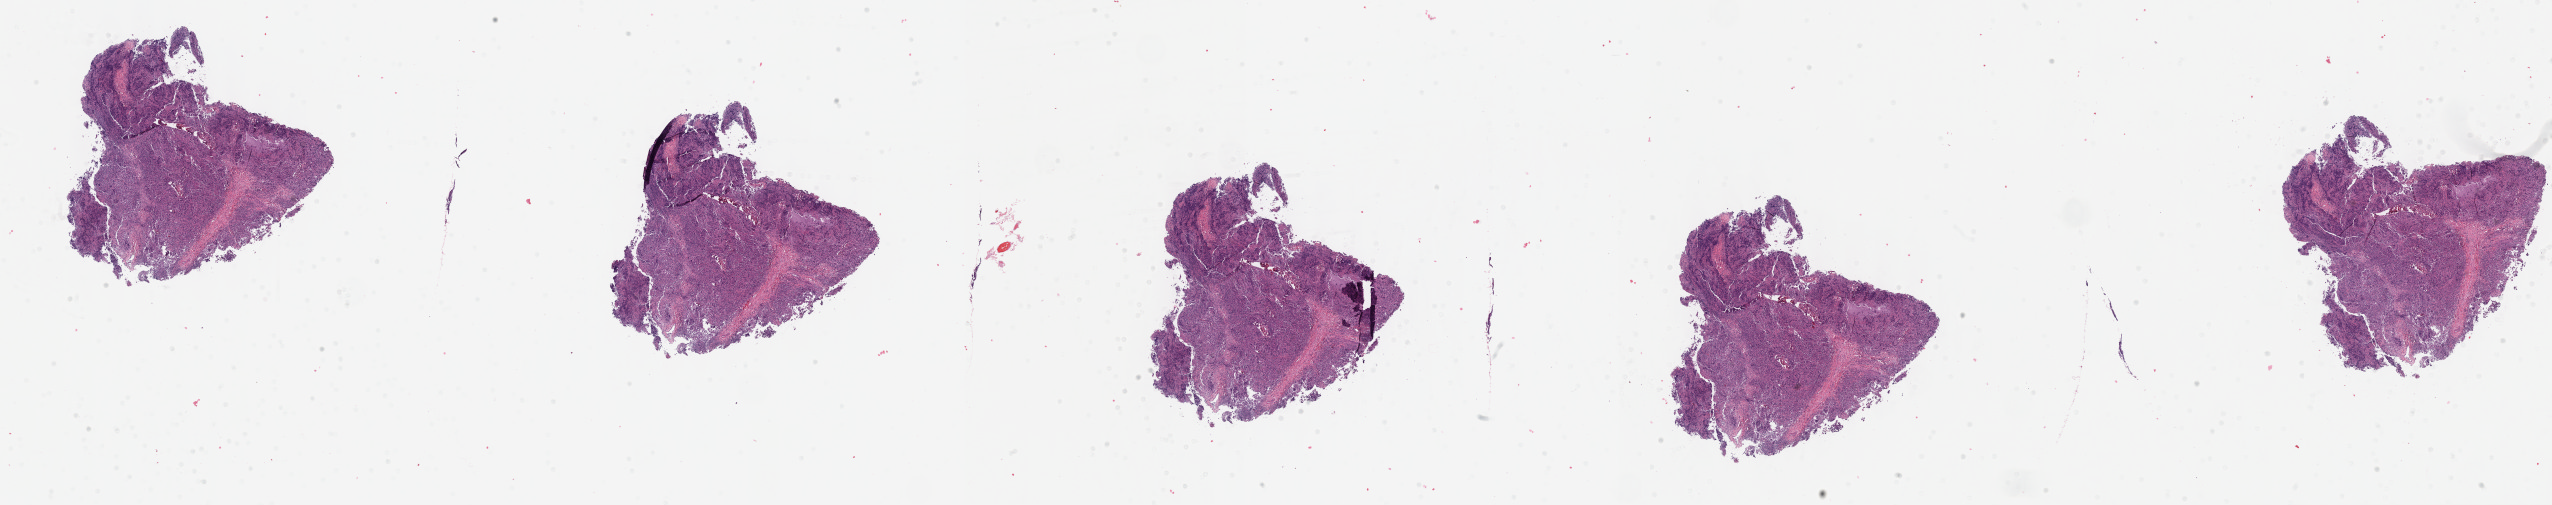
H&E-stained whole-slide image — shown as a low-resolution overview of the whole scanned area (about 41.3 x 8.2 mm, from a 40x scan). Formalin-fixed paraffin-embedded (FFPE) diagnostic section. Testis, primary tumour sample. Male patient; age at initial diagnosis 49 years.
AJCC pathologic stage: I (7th edition). Pathologic diagnosis: Seminoma, NOS. Laterality: left.